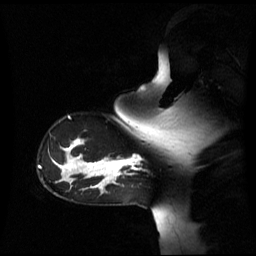
Breast MRI (dynamic contrast-enhanced), one sagittal slice. Slice 46 of 60 in the series (ordered by position). Dynamic contrast-enhanced series, image 2 of 3 at this slice position (ordered by acquisition). 1.5 T. TE 4.2 ms, TR 8.4 ms. 2.6 mm slice thickness. 256 × 256 image matrix, field of view 270 × 270 mm. Female patient, age 39 years. Case-level facts recorded for this patient, not image findings: setting: breast cancer imaged before/during neoadjuvant chemotherapy; receptor status: triple-negative.
Structures marked on this image (semi-automatically segmented with operator editing):
- analysis volume of interest (the breast-tissue region the enhancement analysis was run in; not a lesion): bounding box <105,158,140,179> (left, top, right, bottom; pixels)
- tumour enhancement mask (voxels above the 70 % enhancement threshold inside the analysis volume of interest): <105,158,140,179>